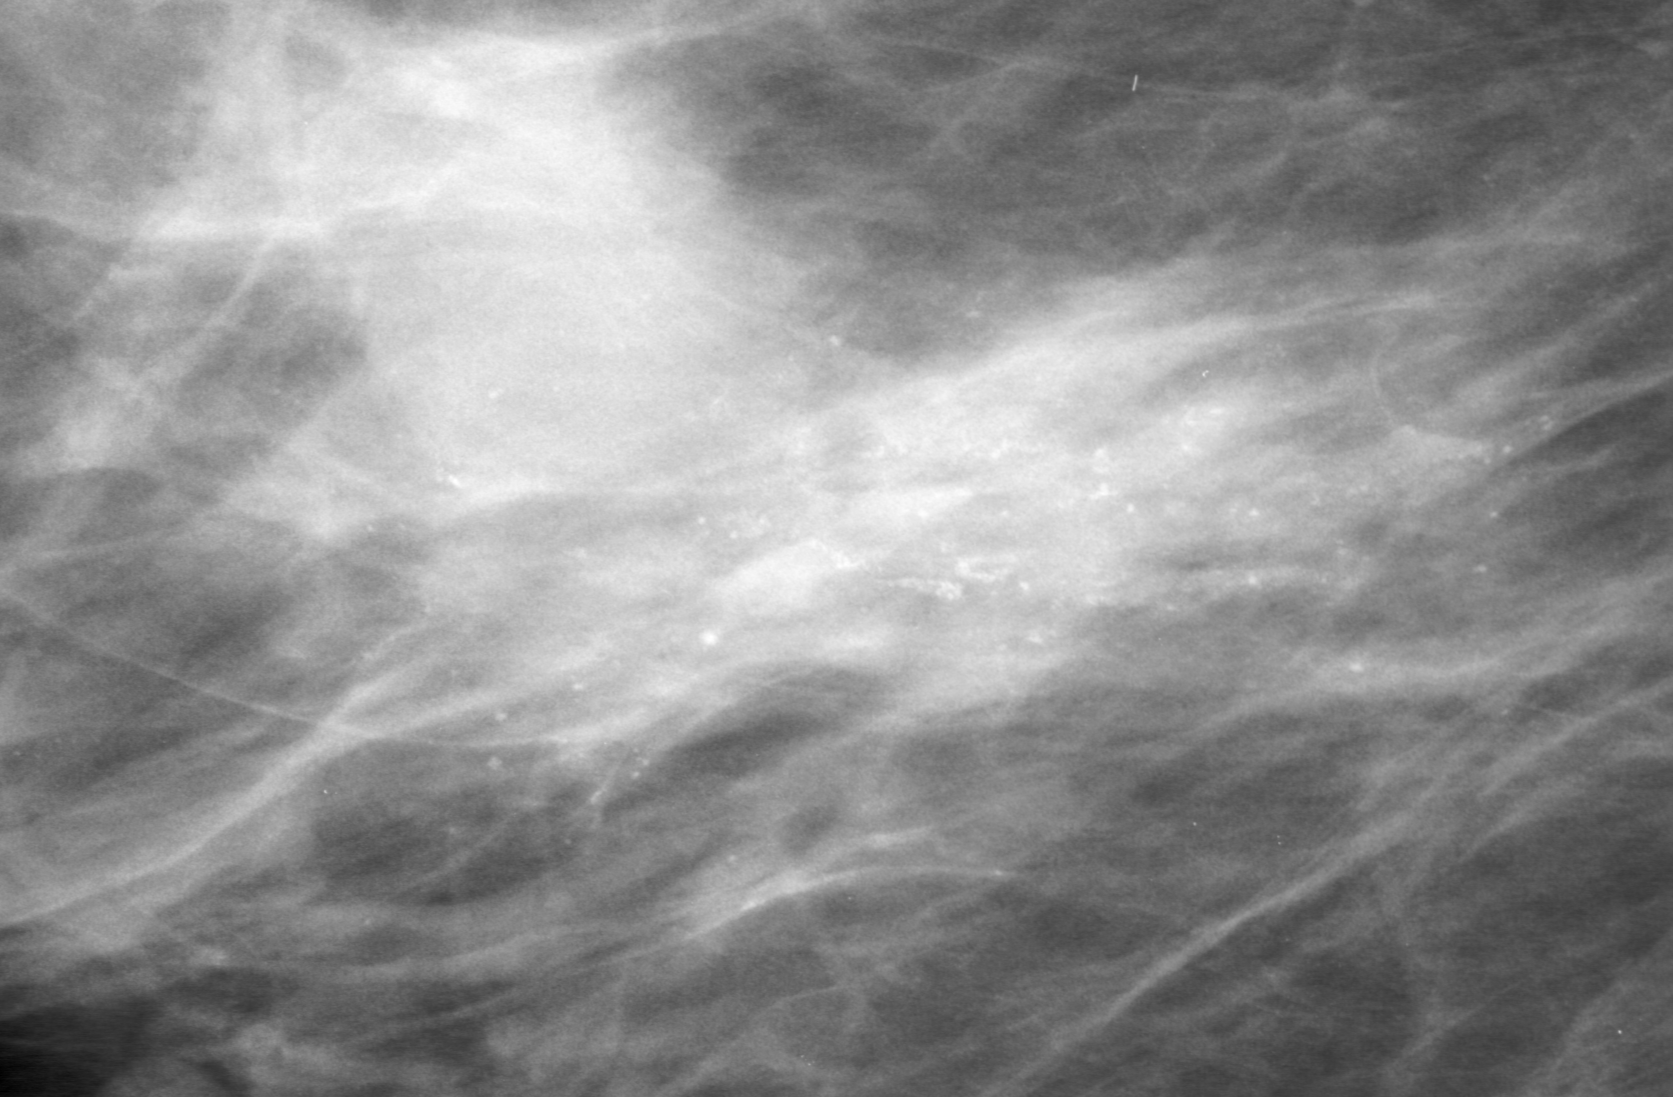
Cropped region of a digitized screen-film mammogram centred on a radiologist-marked abnormality, right breast, MLO view, BI-RADS breast density category 2 (scale 1–4).
- Marked abnormality: calcifications, morphology amorphous / pleomorphic, distribution segmental; BI-RADS assessment category 5; pathology (as recorded): malignant.